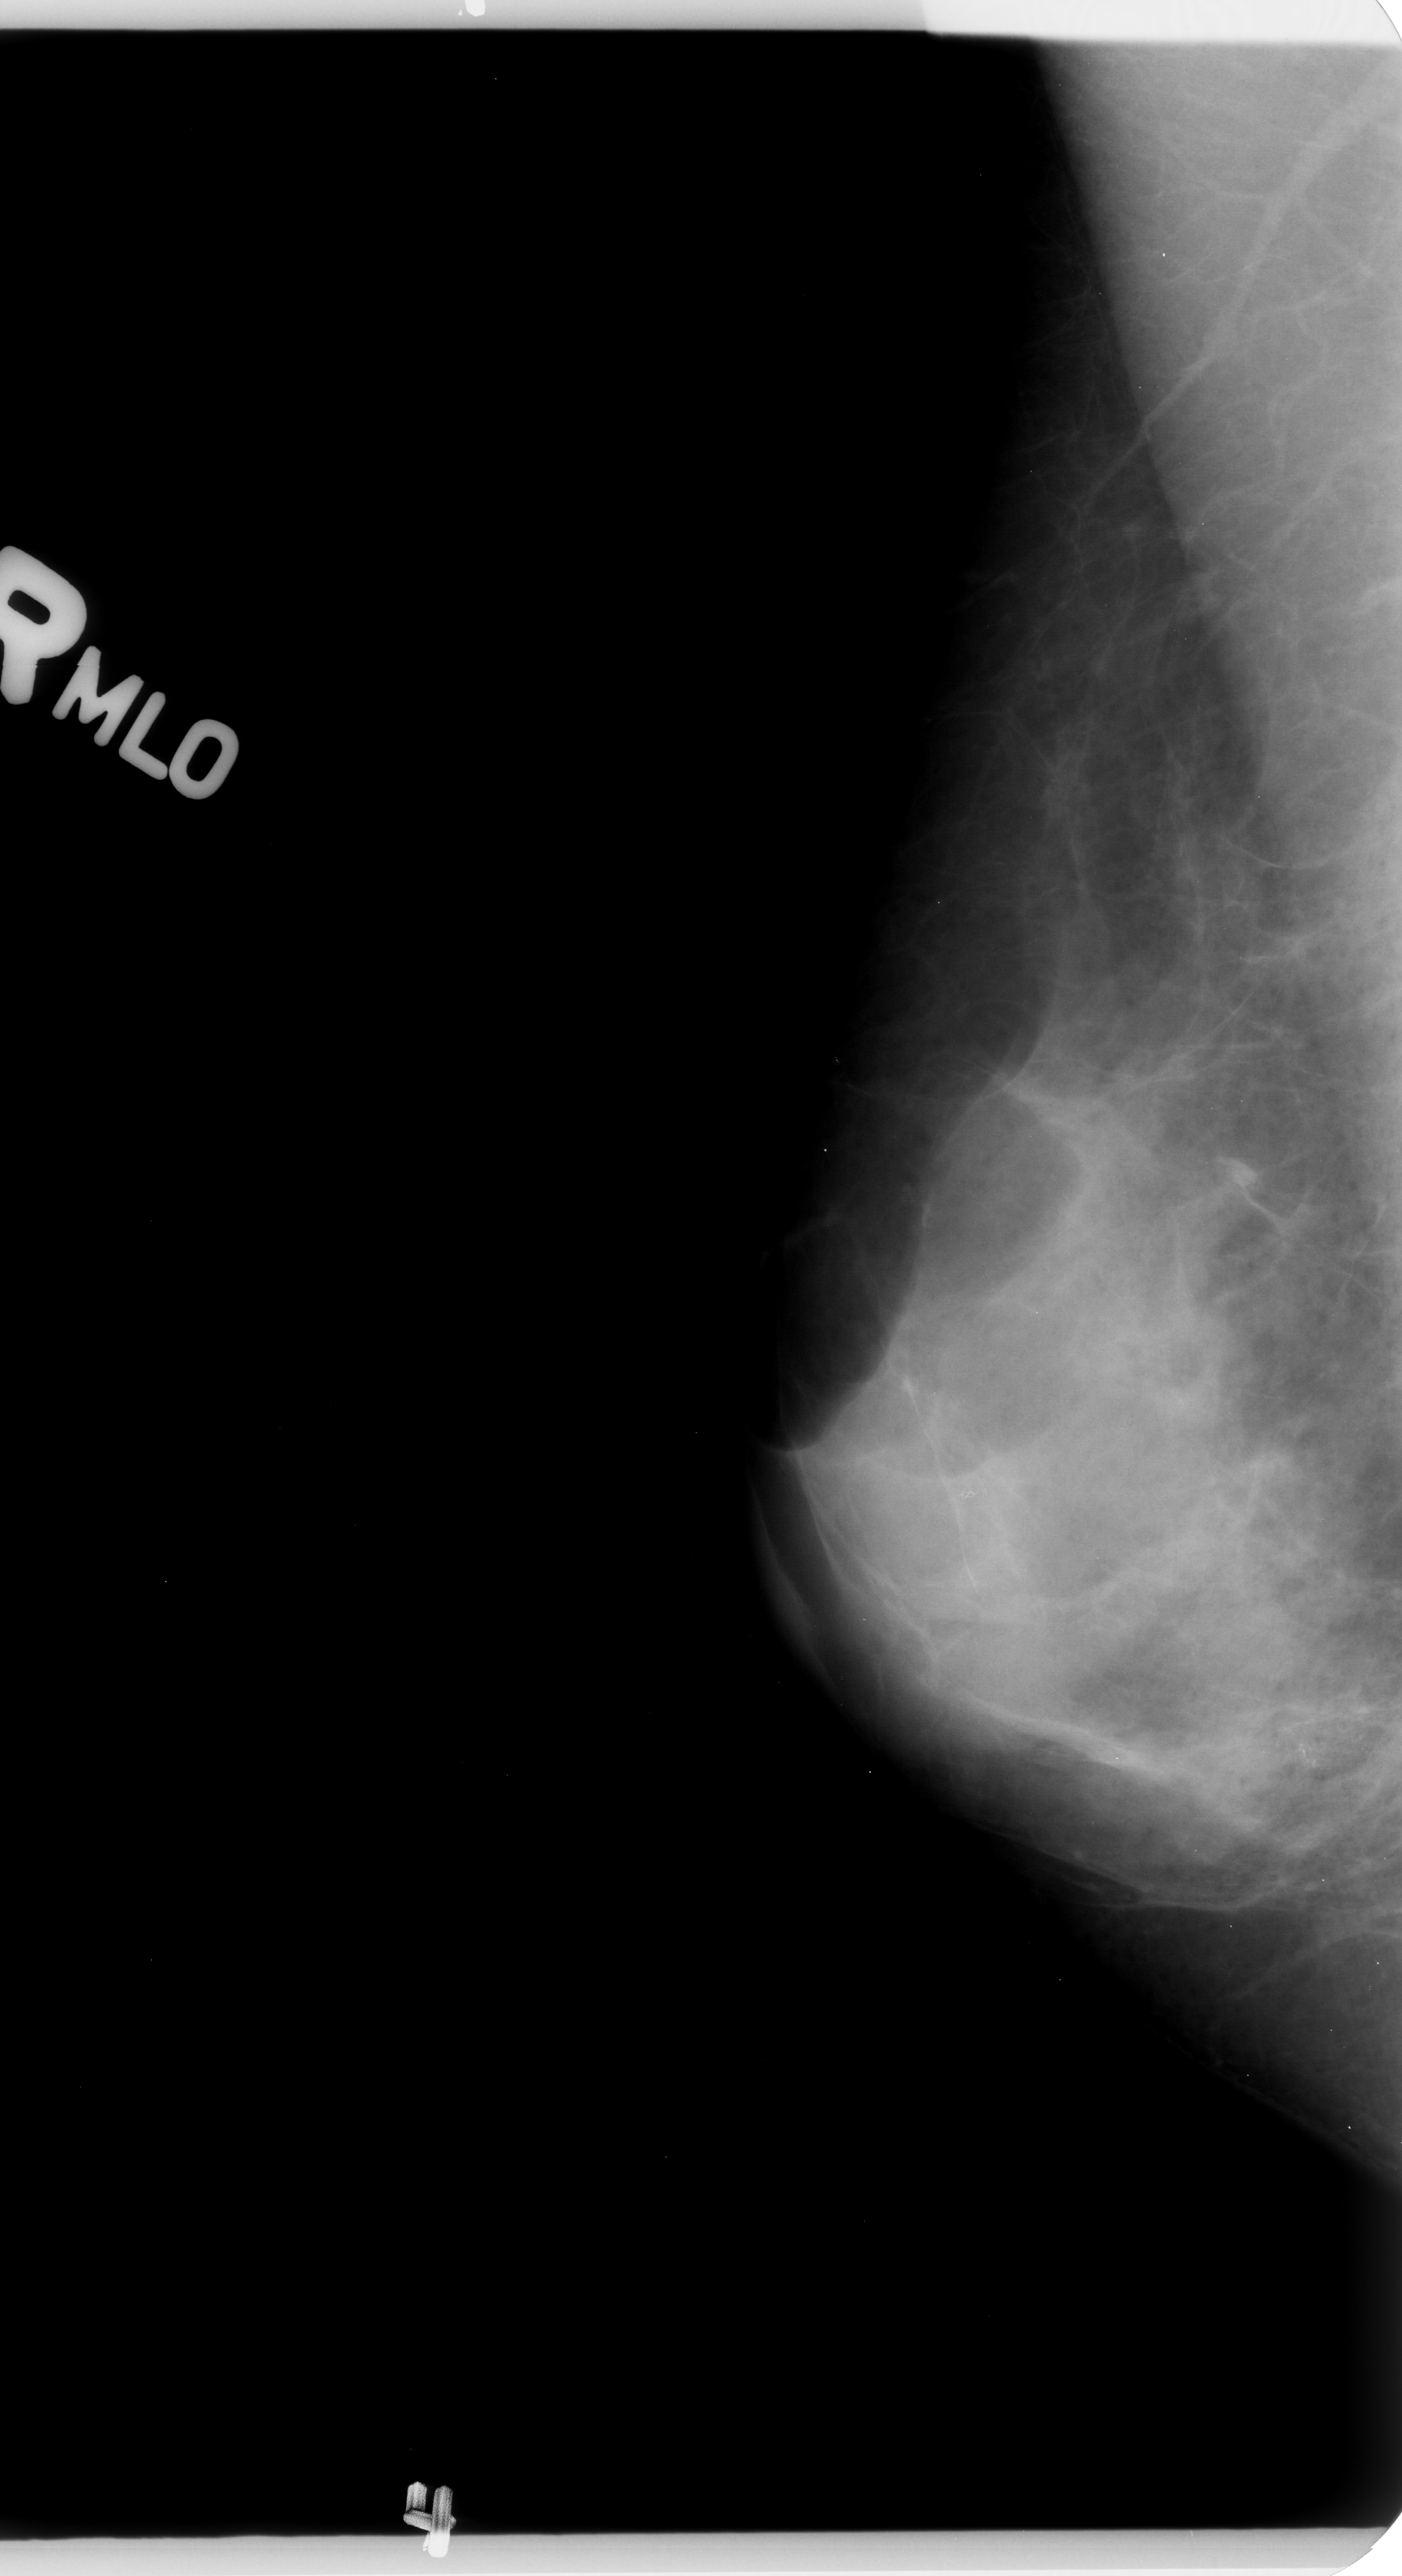
Digitized screen-film mammogram; right breast; mediolateral oblique (MLO) view; BI-RADS breast density category 4 (scale 1–4); 1402 × 2576 image matrix.
Marked abnormalities (boxes around the expert regions of interest):
- calcifications, morphology pleomorphic, distribution clustered; BI-RADS assessment category 4; pathology result (as recorded, not read from the image): benign: bounding box (x1, y1, x2, y2) in pixels: (1249, 1680, 1364, 1796)